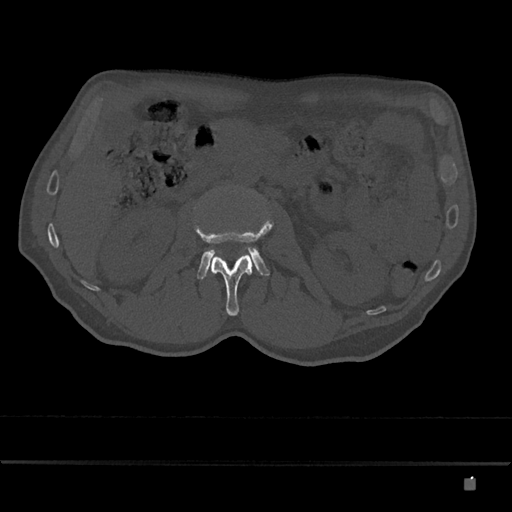
CT including the spine, one axial slice; position 453 of 797 along the scan axis; reconstruction kernel Br40s/3; 120 kVp; bone window (W 1800 / L 400 HU); 0.5 mm slice thickness; 512 × 512 image matrix, field of view 390 × 390 mm. Patient: male, 72 years. Case-level facts recorded for this patient, not image findings: primary cancer: prostate.
Annotated regions visible in this slice (semi-automatically segmented with operator editing):
- L2 vertebra: box from (x=196, y=221) to (x=274, y=316) px
- L3 vertebra: (x=194, y=207)–(x=270, y=280)